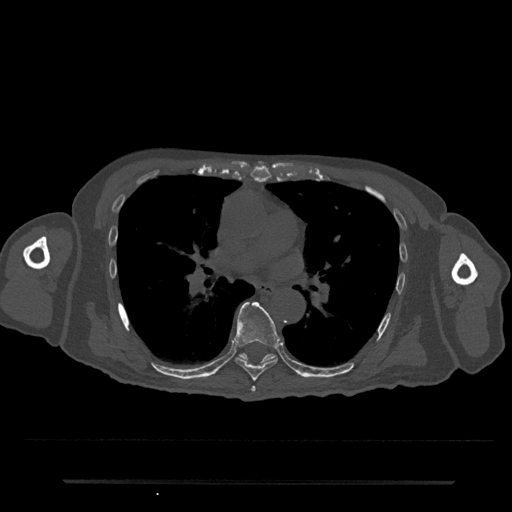
CT including the spine, one axial slice; slice 465 of 797 in the series (ordered by position); reconstruction kernel Br40s/3; 120 kVp; bone window (W 1800 / L 400 HU); 0.5 mm slice thickness; 512 × 512 image matrix, field of view 427 × 427 mm. Male patient, age 74 years. Case-level facts recorded for this patient, not image findings: primary cancer: prostate.
Structures marked on this image (semi-automatic segmentation, software-assisted and operator-edited):
- T6 vertebra: bounding box [x1, y1, x2, y2] px = [251, 386, 256, 392]
- T7 vertebra: [233, 302, 280, 382]
- T8 vertebra: [239, 353, 276, 362]